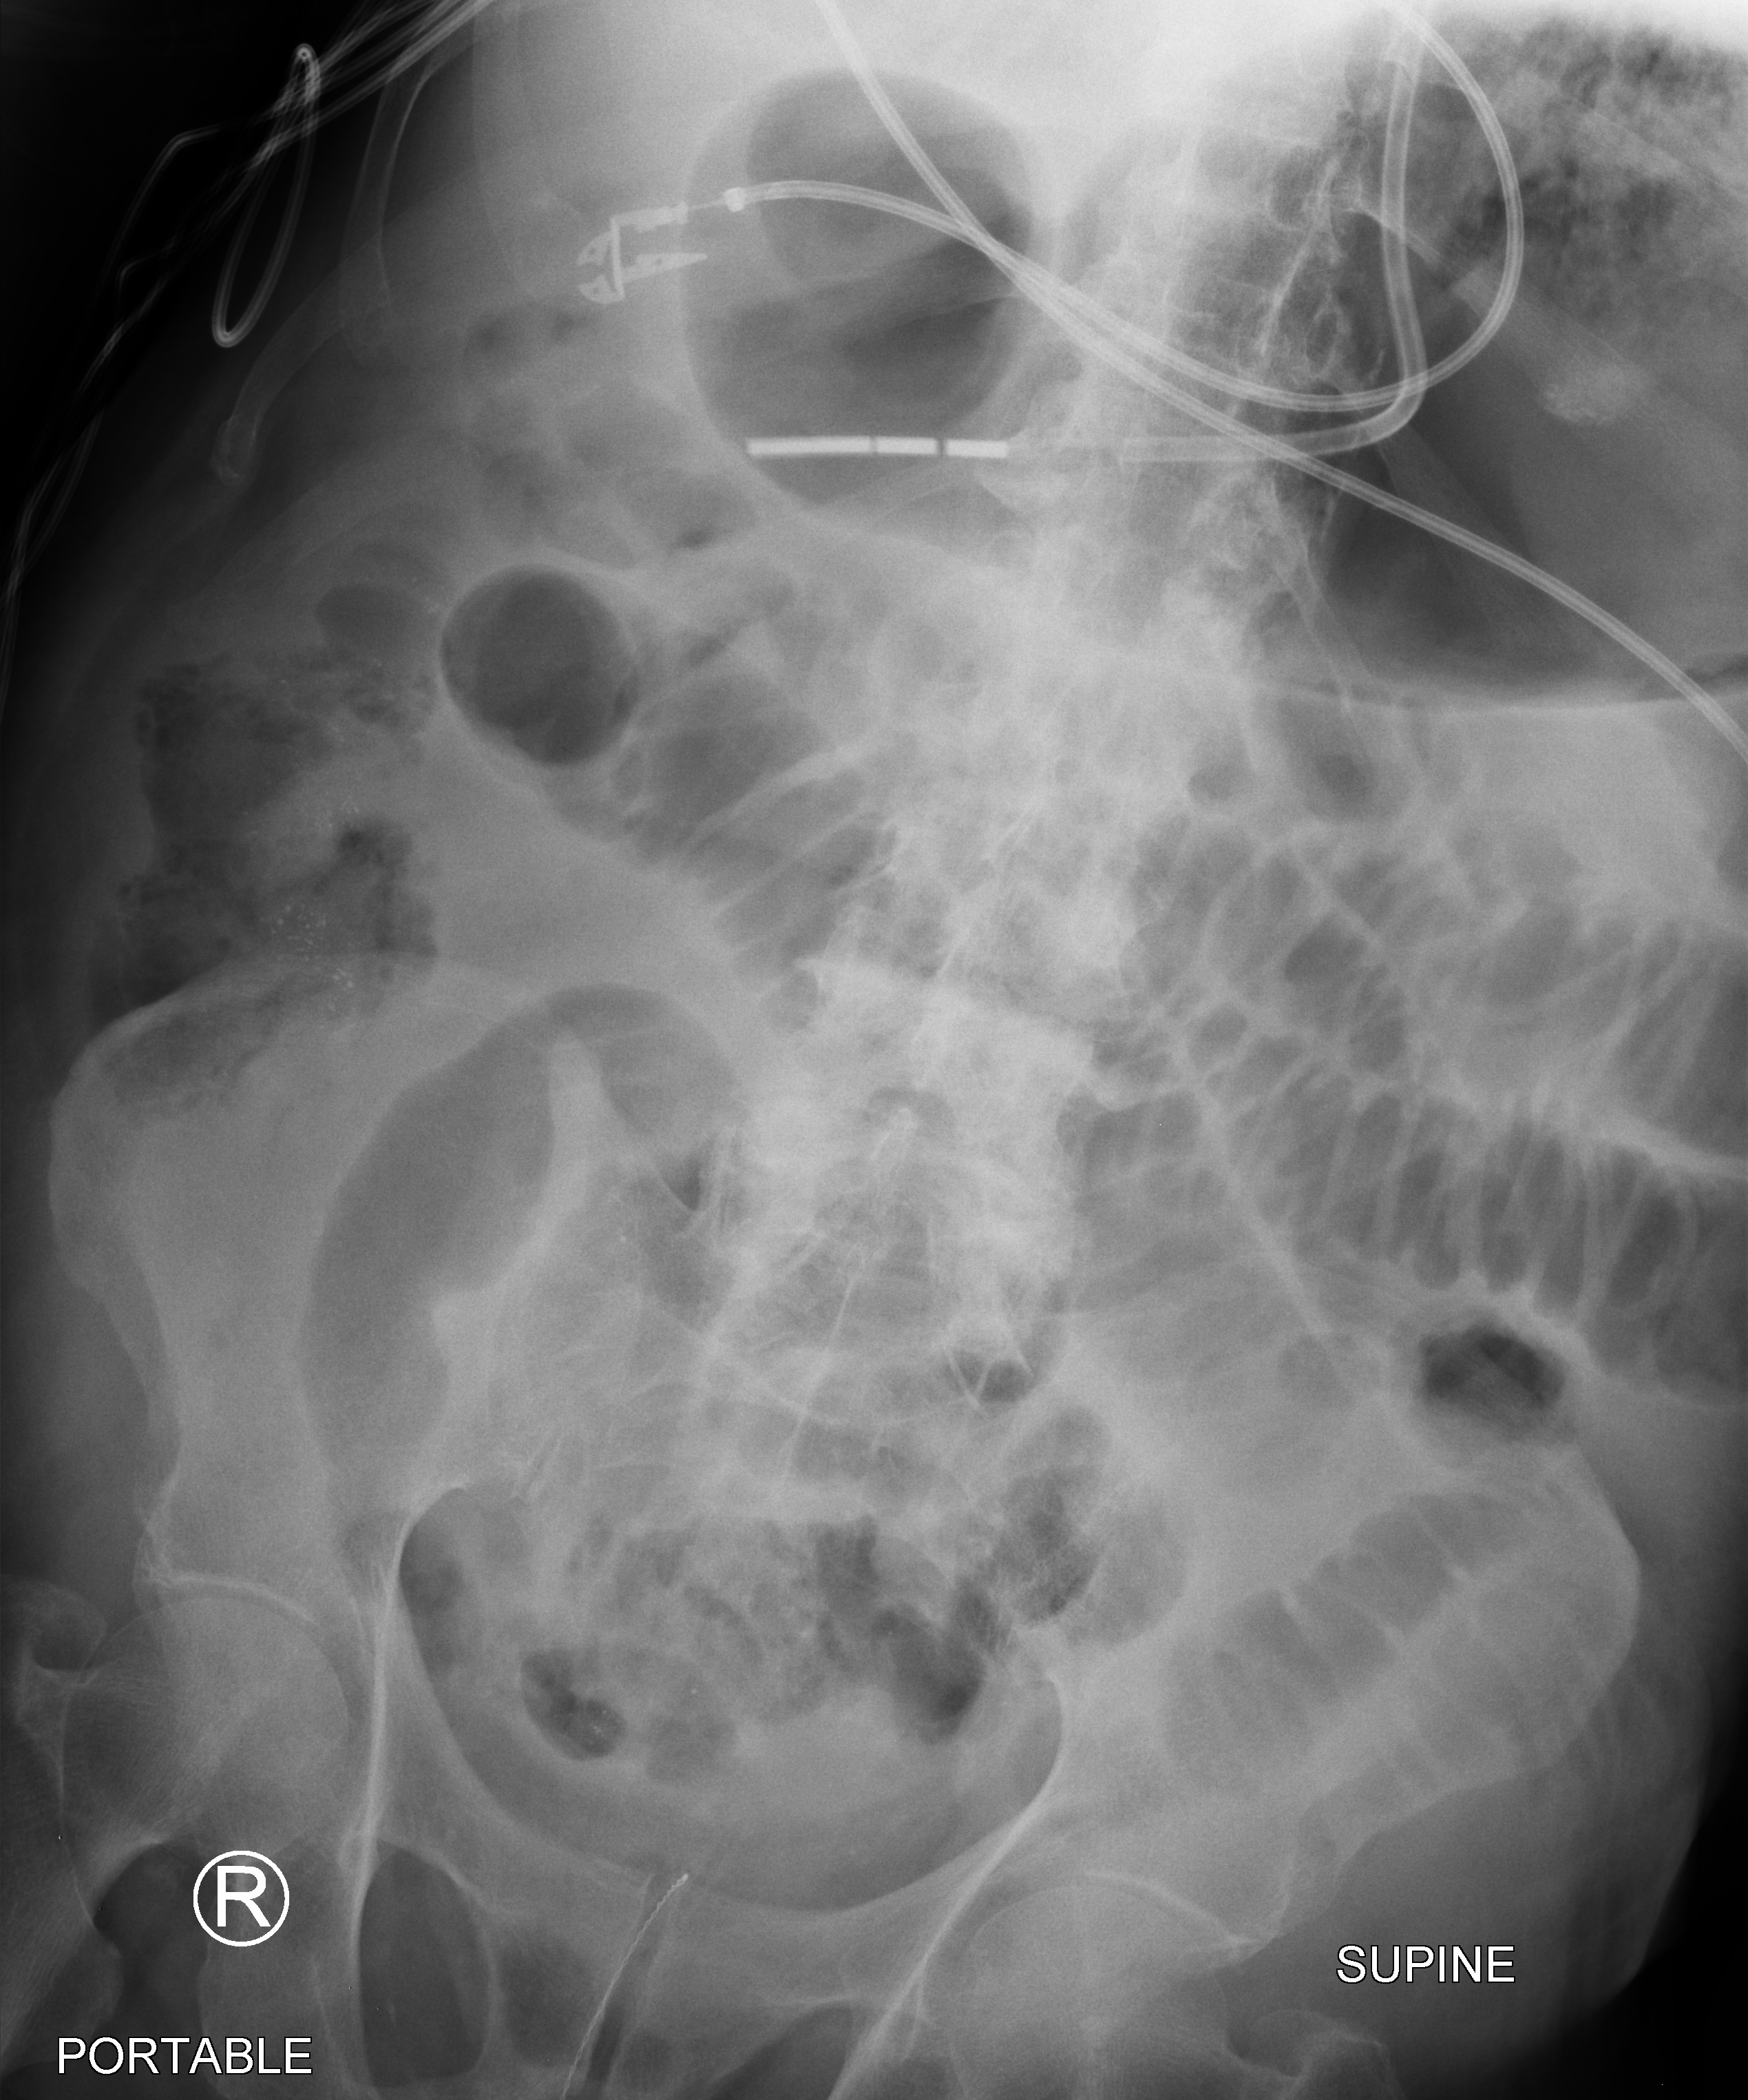
Bedside abdomen radiograph (computed radiography), anteroposterior (AP) projection. Patient hospitalised with COVID-19; male, aged 75–90 years.
Hospital-stay facts (about this admission, not read from this image; timing relative to this image not recorded): mechanically ventilated during this hospital stay: yes.